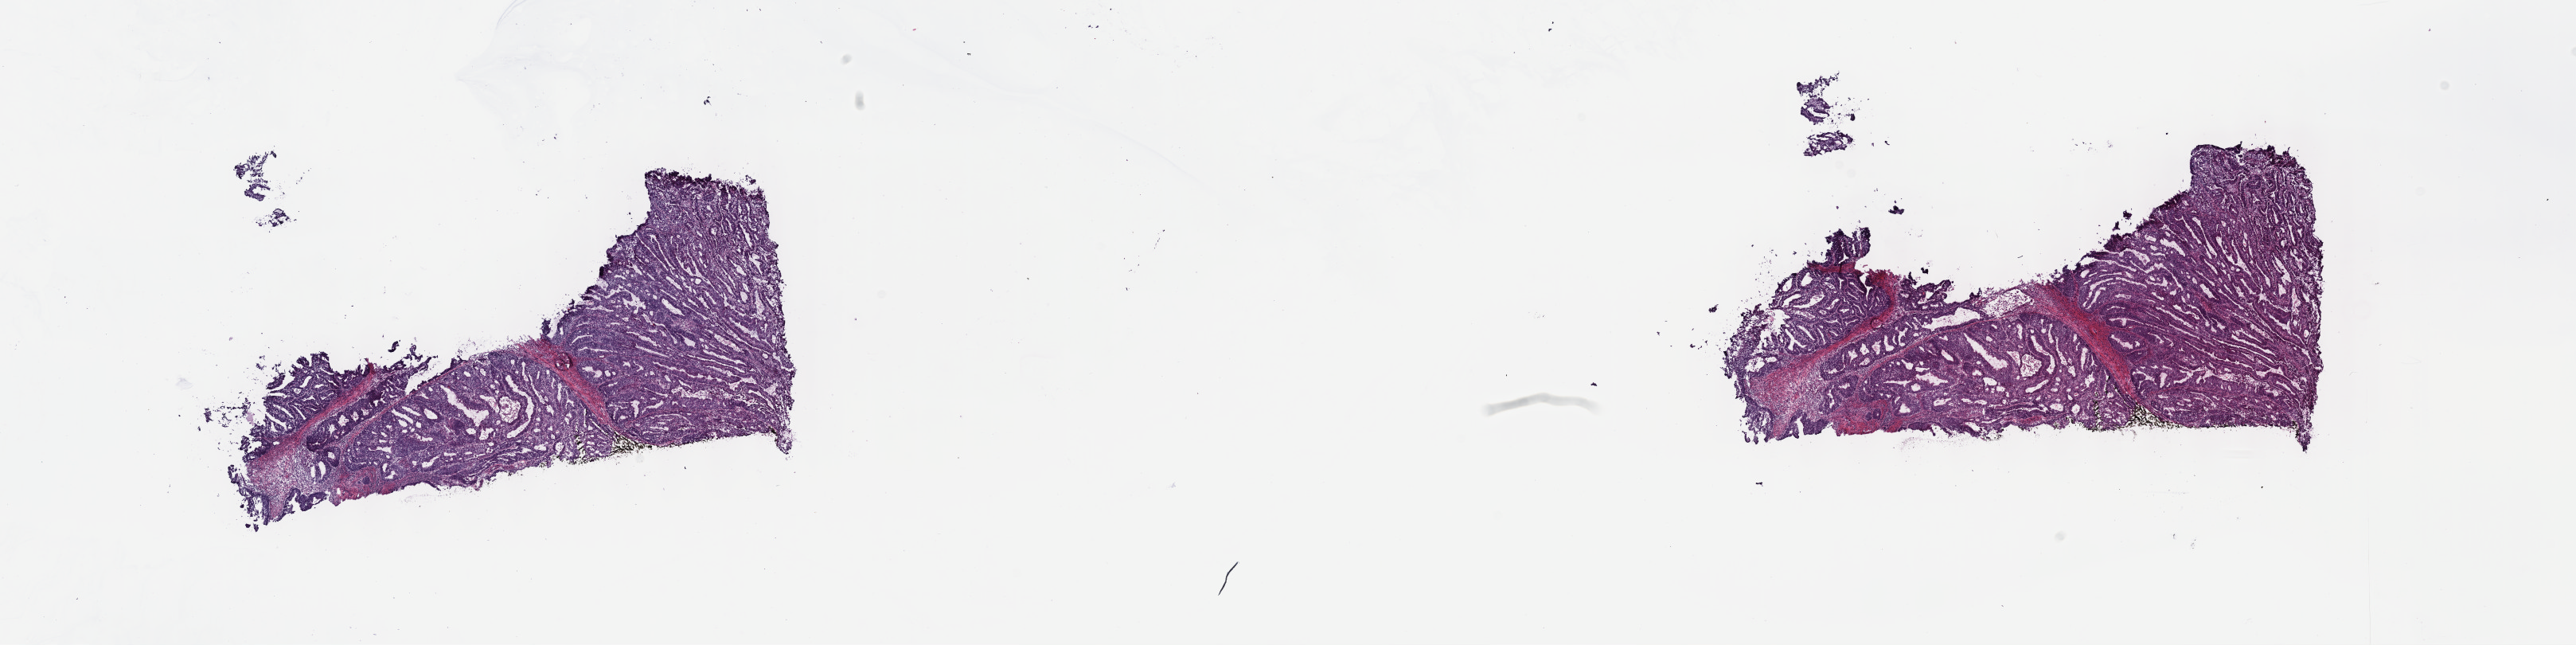
H&E whole-slide image — shown as a low-resolution overview of the whole scanned area (about 26.2 x 6.6 mm, slide scanned at 40x), frozen section from the top of the tissue portion, primary tumour sample from the uterus. Female patient; age at initial diagnosis 58 years. Histologic grade: G2 (moderately differentiated). Slide review estimates, as recorded: tumour cells 60%, tumour nuclei 60%, normal cells 10%, stromal cells 30%, necrosis 0%. Infiltration values recorded for this section: lymphocyte infiltration 5%, monocyte infiltration 5%, neutrophil infiltration 0%.
Diagnosis: Endometrioid adenocarcinoma, NOS (endometrium). FIGO stage: IB.